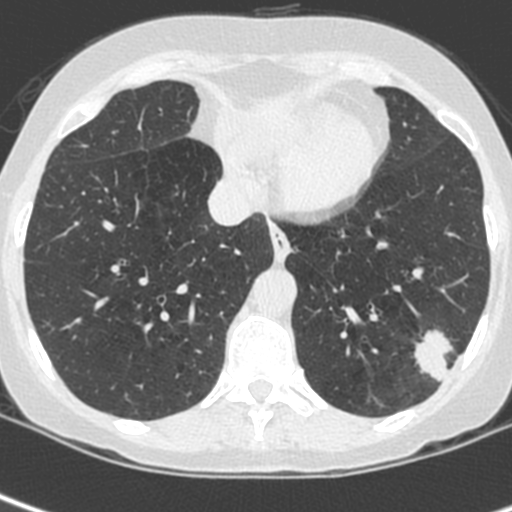
Axial slice from a low-dose chest CT screening exam; baseline screening round; lung window (W 1500 / L -600 HU); slice 165 of 252 in the series. Female participant, aged 56 years at enrolment.
Lesion marked by an expert reader, bounding box (x1, y1, x2, y2) in pixels: (409, 326, 473, 389). The exam's reader record, not a measurement of the box and not confirmed to be the same lesion: non-calcified nodule or mass ≥4 mm, left lower lobe, 37 × 29 mm, spiculated (stellate) margins, ground glass attenuation.